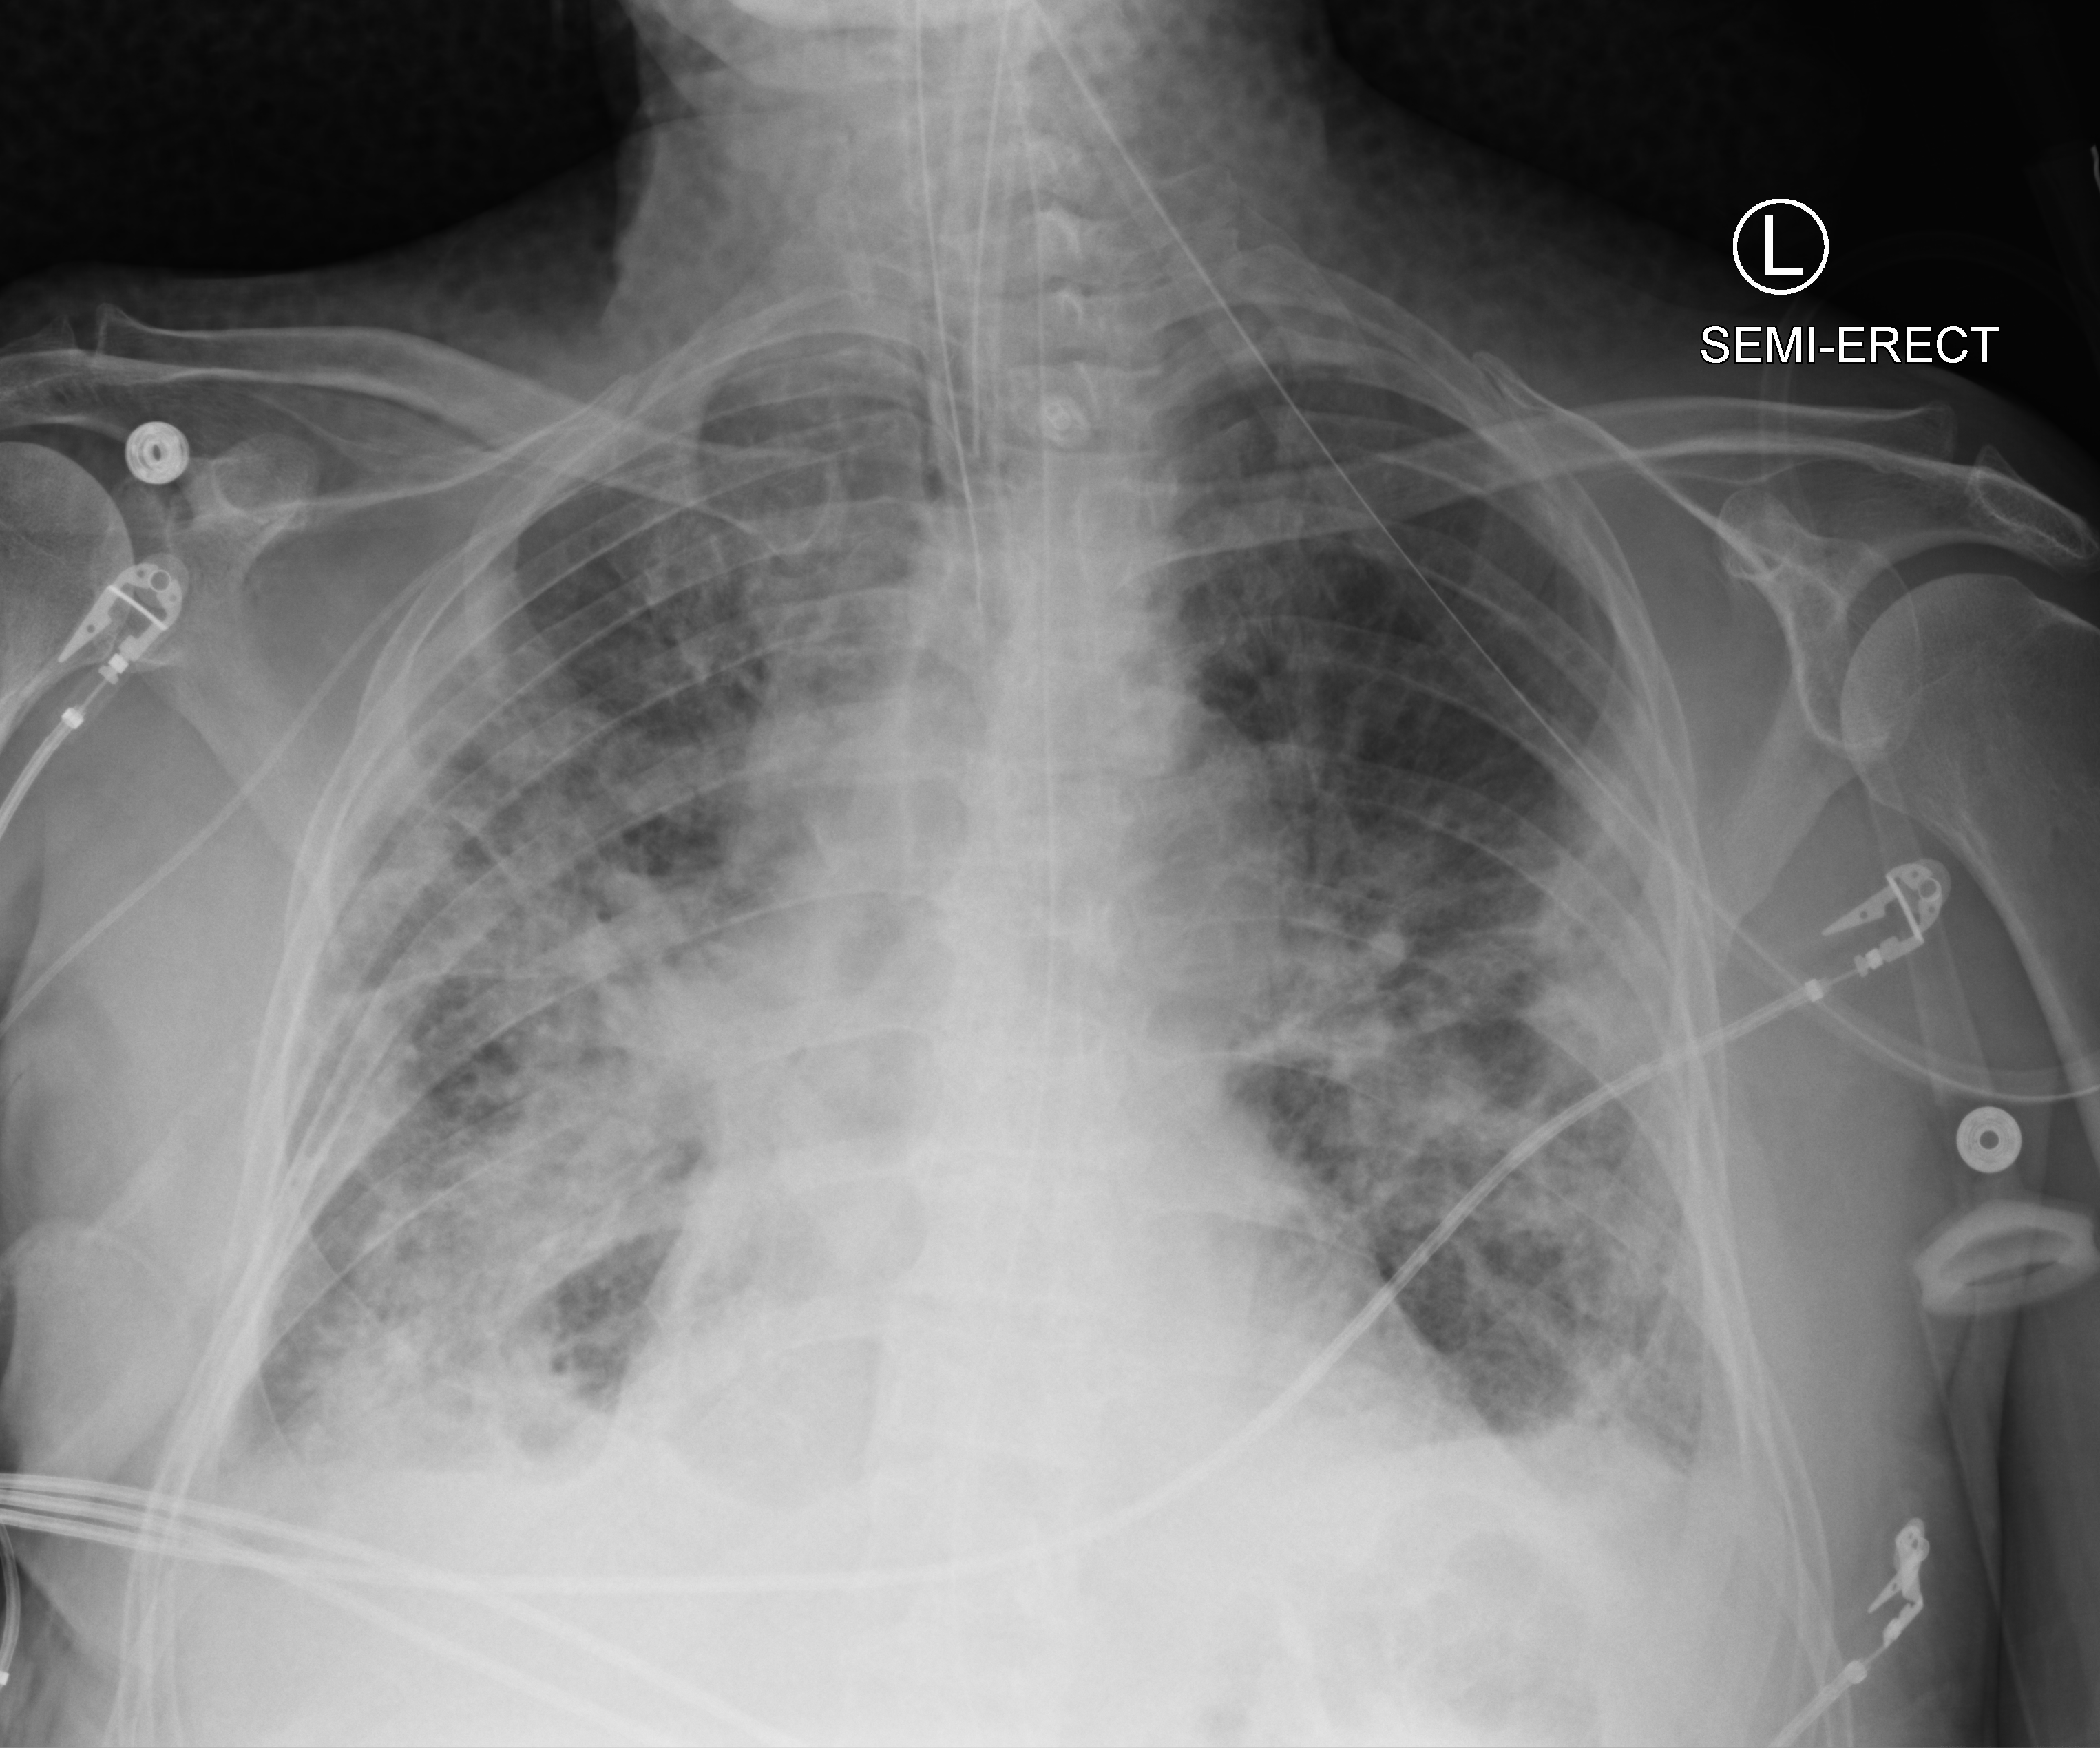
Bedside chest radiograph (computed radiography), anteroposterior (AP) projection. Male patient hospitalised with COVID-19, age 75–90 years.
Hospital-stay facts (about this admission, not read from this image; timing relative to this image not recorded):
- mechanically ventilated during this hospital stay: yes